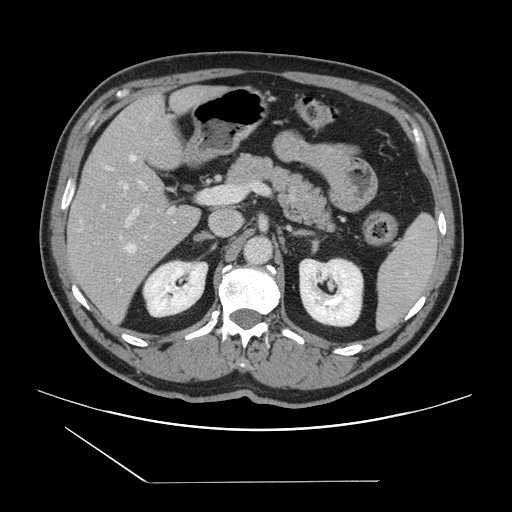
Contrast-enhanced abdominal CT, one axial slice. Position 79 of 157 along the scan axis. Intravenous contrast given. Soft-tissue window (W 400 / L 40 HU). 2.5 mm slice thickness. 512 × 512 image matrix. Male patient, age 61 years. Case-level facts recorded for this patient, not image findings: diagnosis: colorectal cancer liver metastases, imaged before liver resection; multiple liver metastases: yes; largest metastasis: 5.5 cm; chemotherapy before resection: no.
Outlined on this slice (outlined manually by an expert reader):
- hepatic veins: bounding box (x1, y1, x2, y2) in pixels: (108, 155, 136, 252)
- liver: (68, 87, 219, 329)
- planned liver remnant (the part of the liver to remain after resection): (70, 87, 218, 220)
- portal vein (with intrahepatic branches): (102, 181, 174, 226)